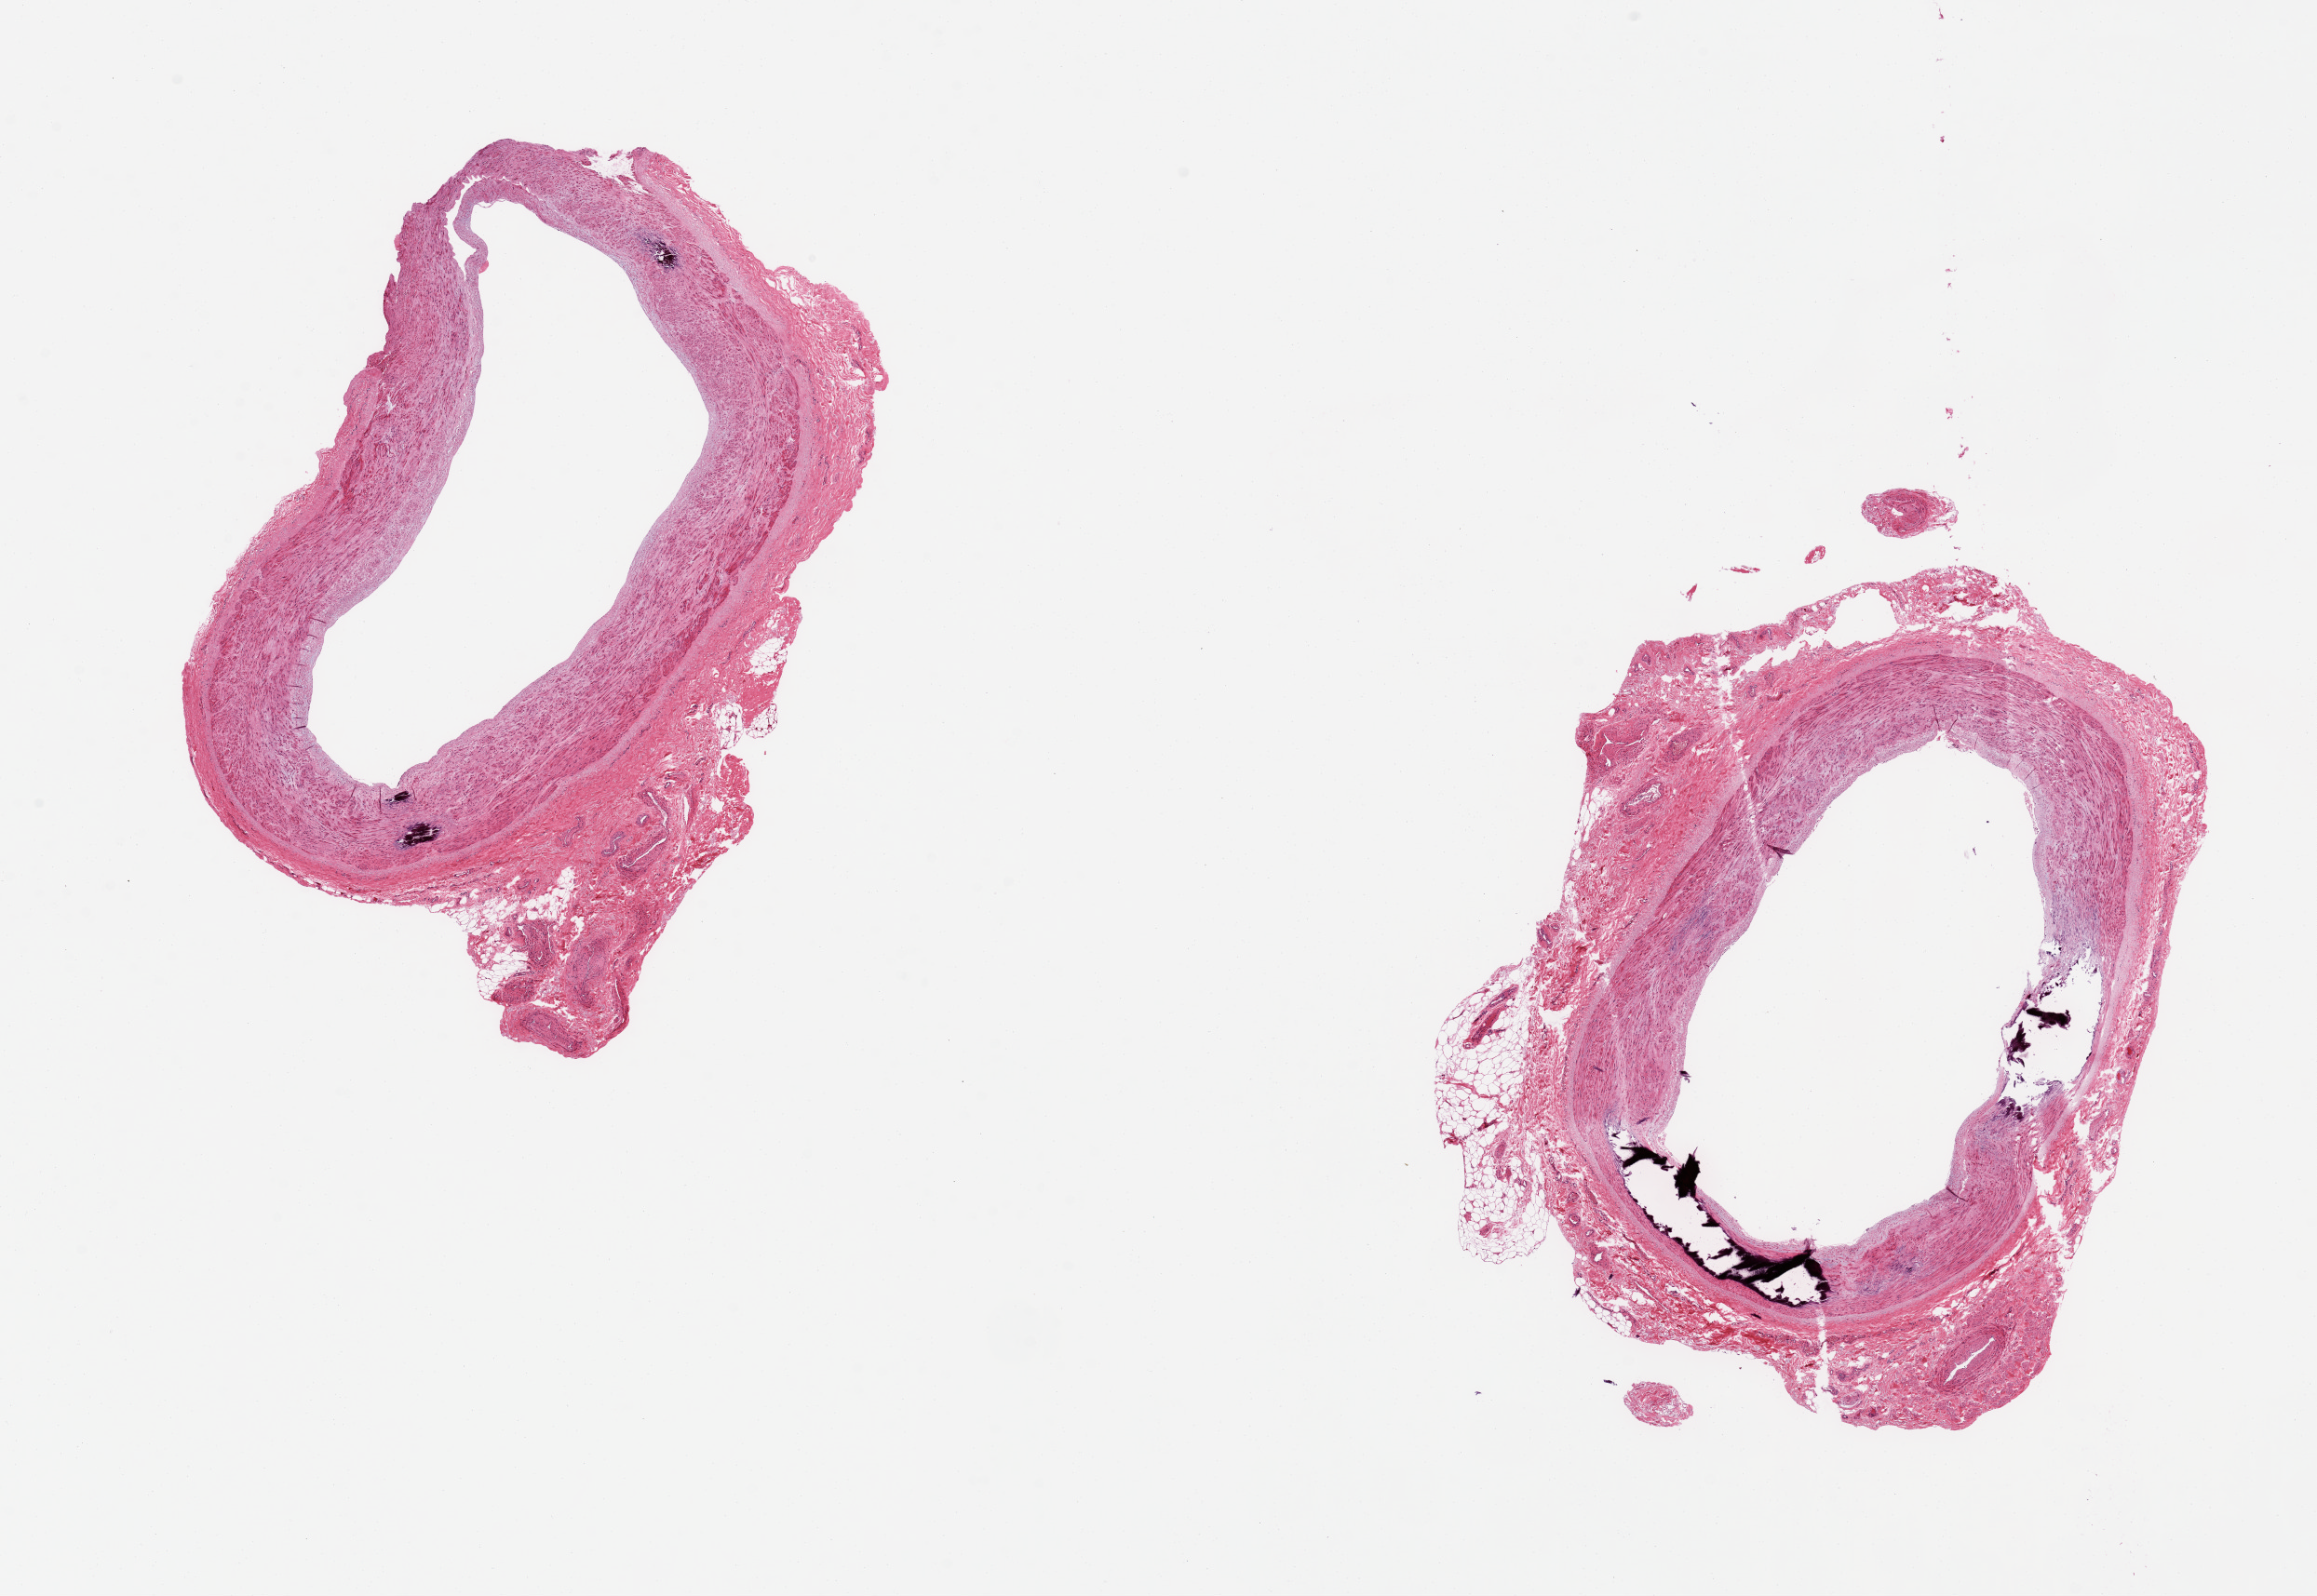
Digitized haematoxylin and eosin-stained section, whole scanned area (about 19.7 x 13.6 mm, acquisition: 20x scan) shown as a low-resolution overview. PAXgene-fixed, paraffin-embedded tissue. Target tissue: tibial artery. Donor tissue sample.
Pathologist's review note for this sample: 4 x 6.5mm specimen. Foci of Monckeberg???s medial sclerosis.